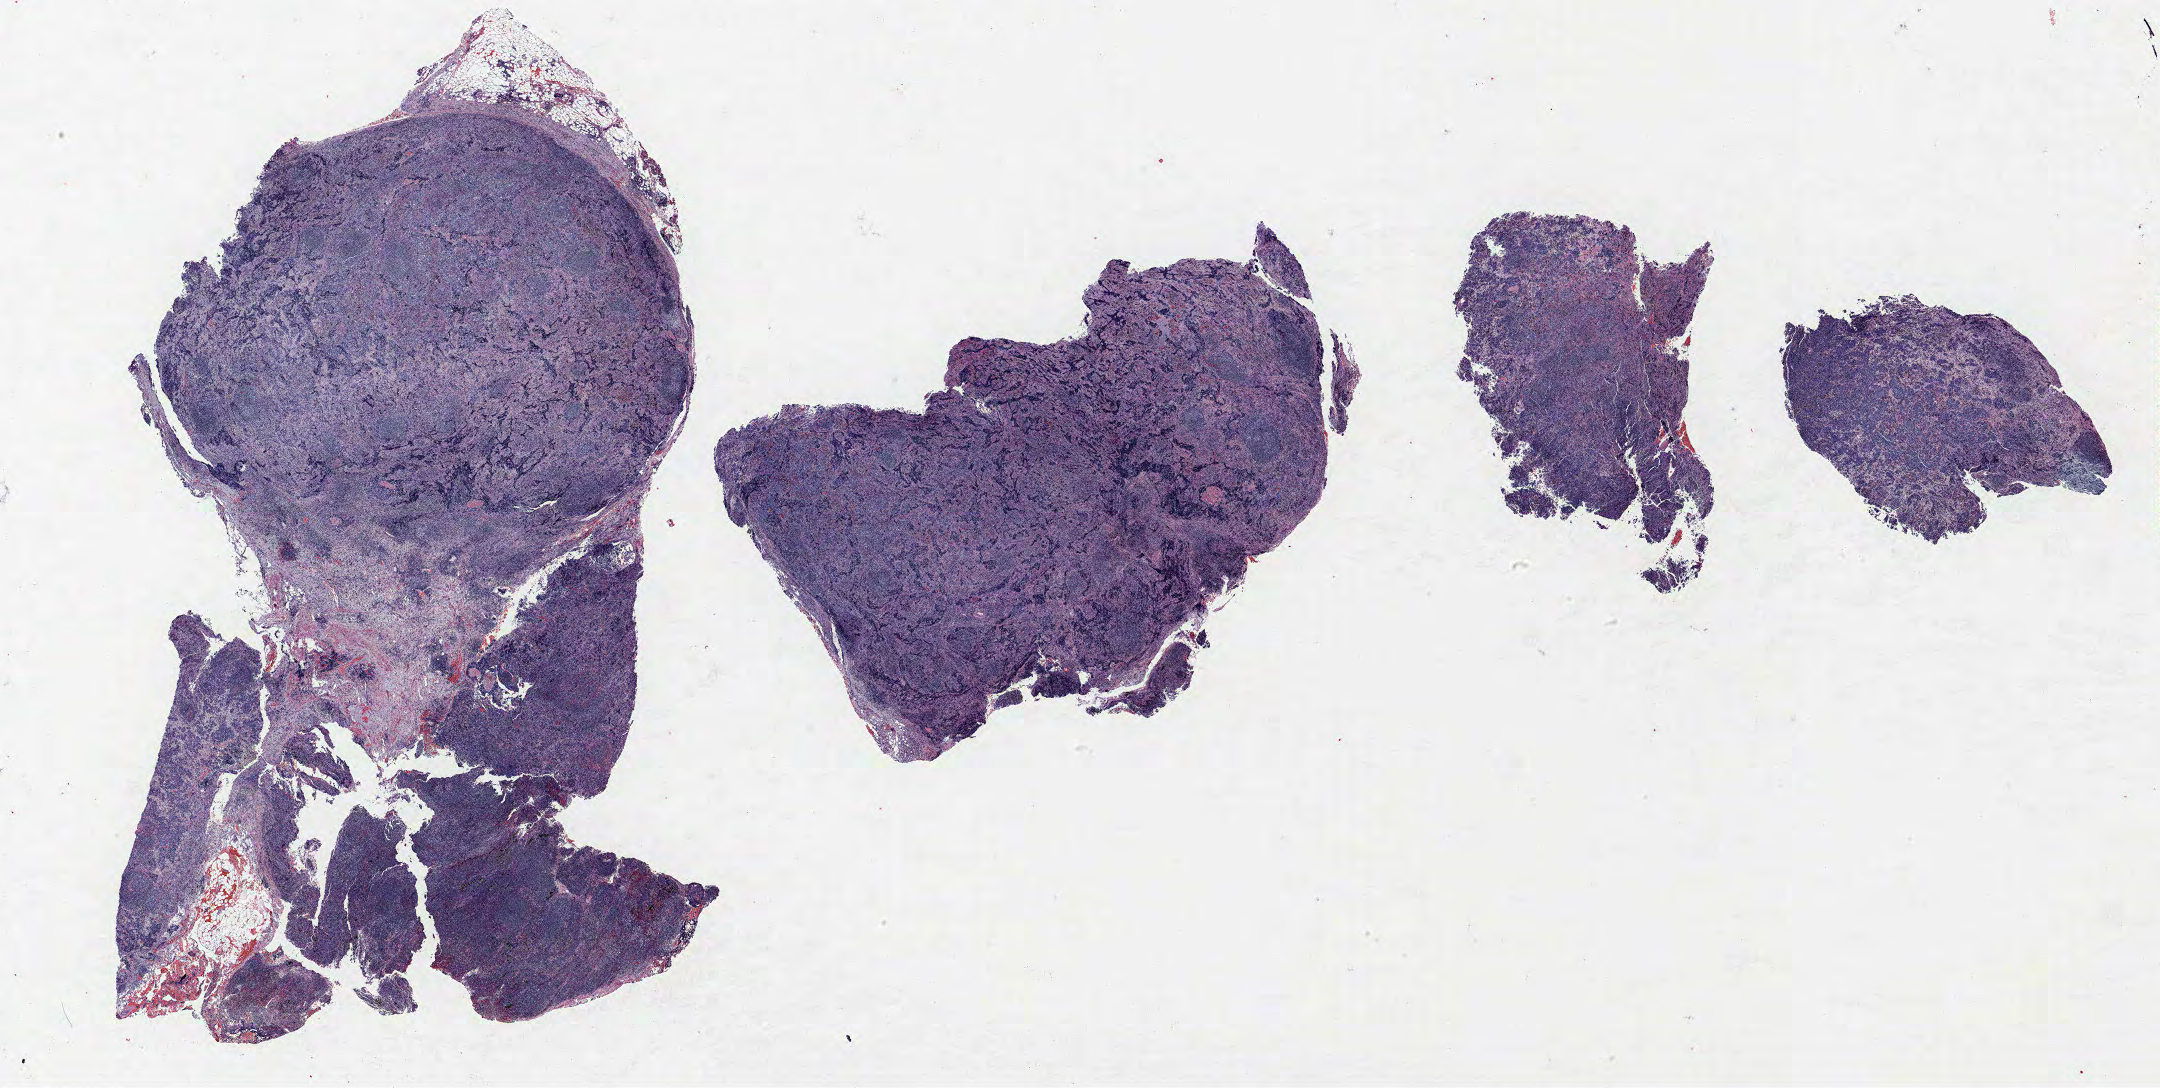
Hematoxylin and eosin (H&E) stained whole-slide image — a low-resolution overview of the entire scanned area, about 34.6 x 17.4 mm (acquisition: 40x scan). Formalin-fixed paraffin-embedded (FFPE) section. Lung. Female, age 55 at enrolment. Current smoker at enrolment.
Tumour size (pathology): 24 mm. Stage (AJCC 6th edition): IIB. Participant's lung-cancer diagnosis: Small cell carcinoma, NOS. Primary tumour location (clinical record): right middle lobe.